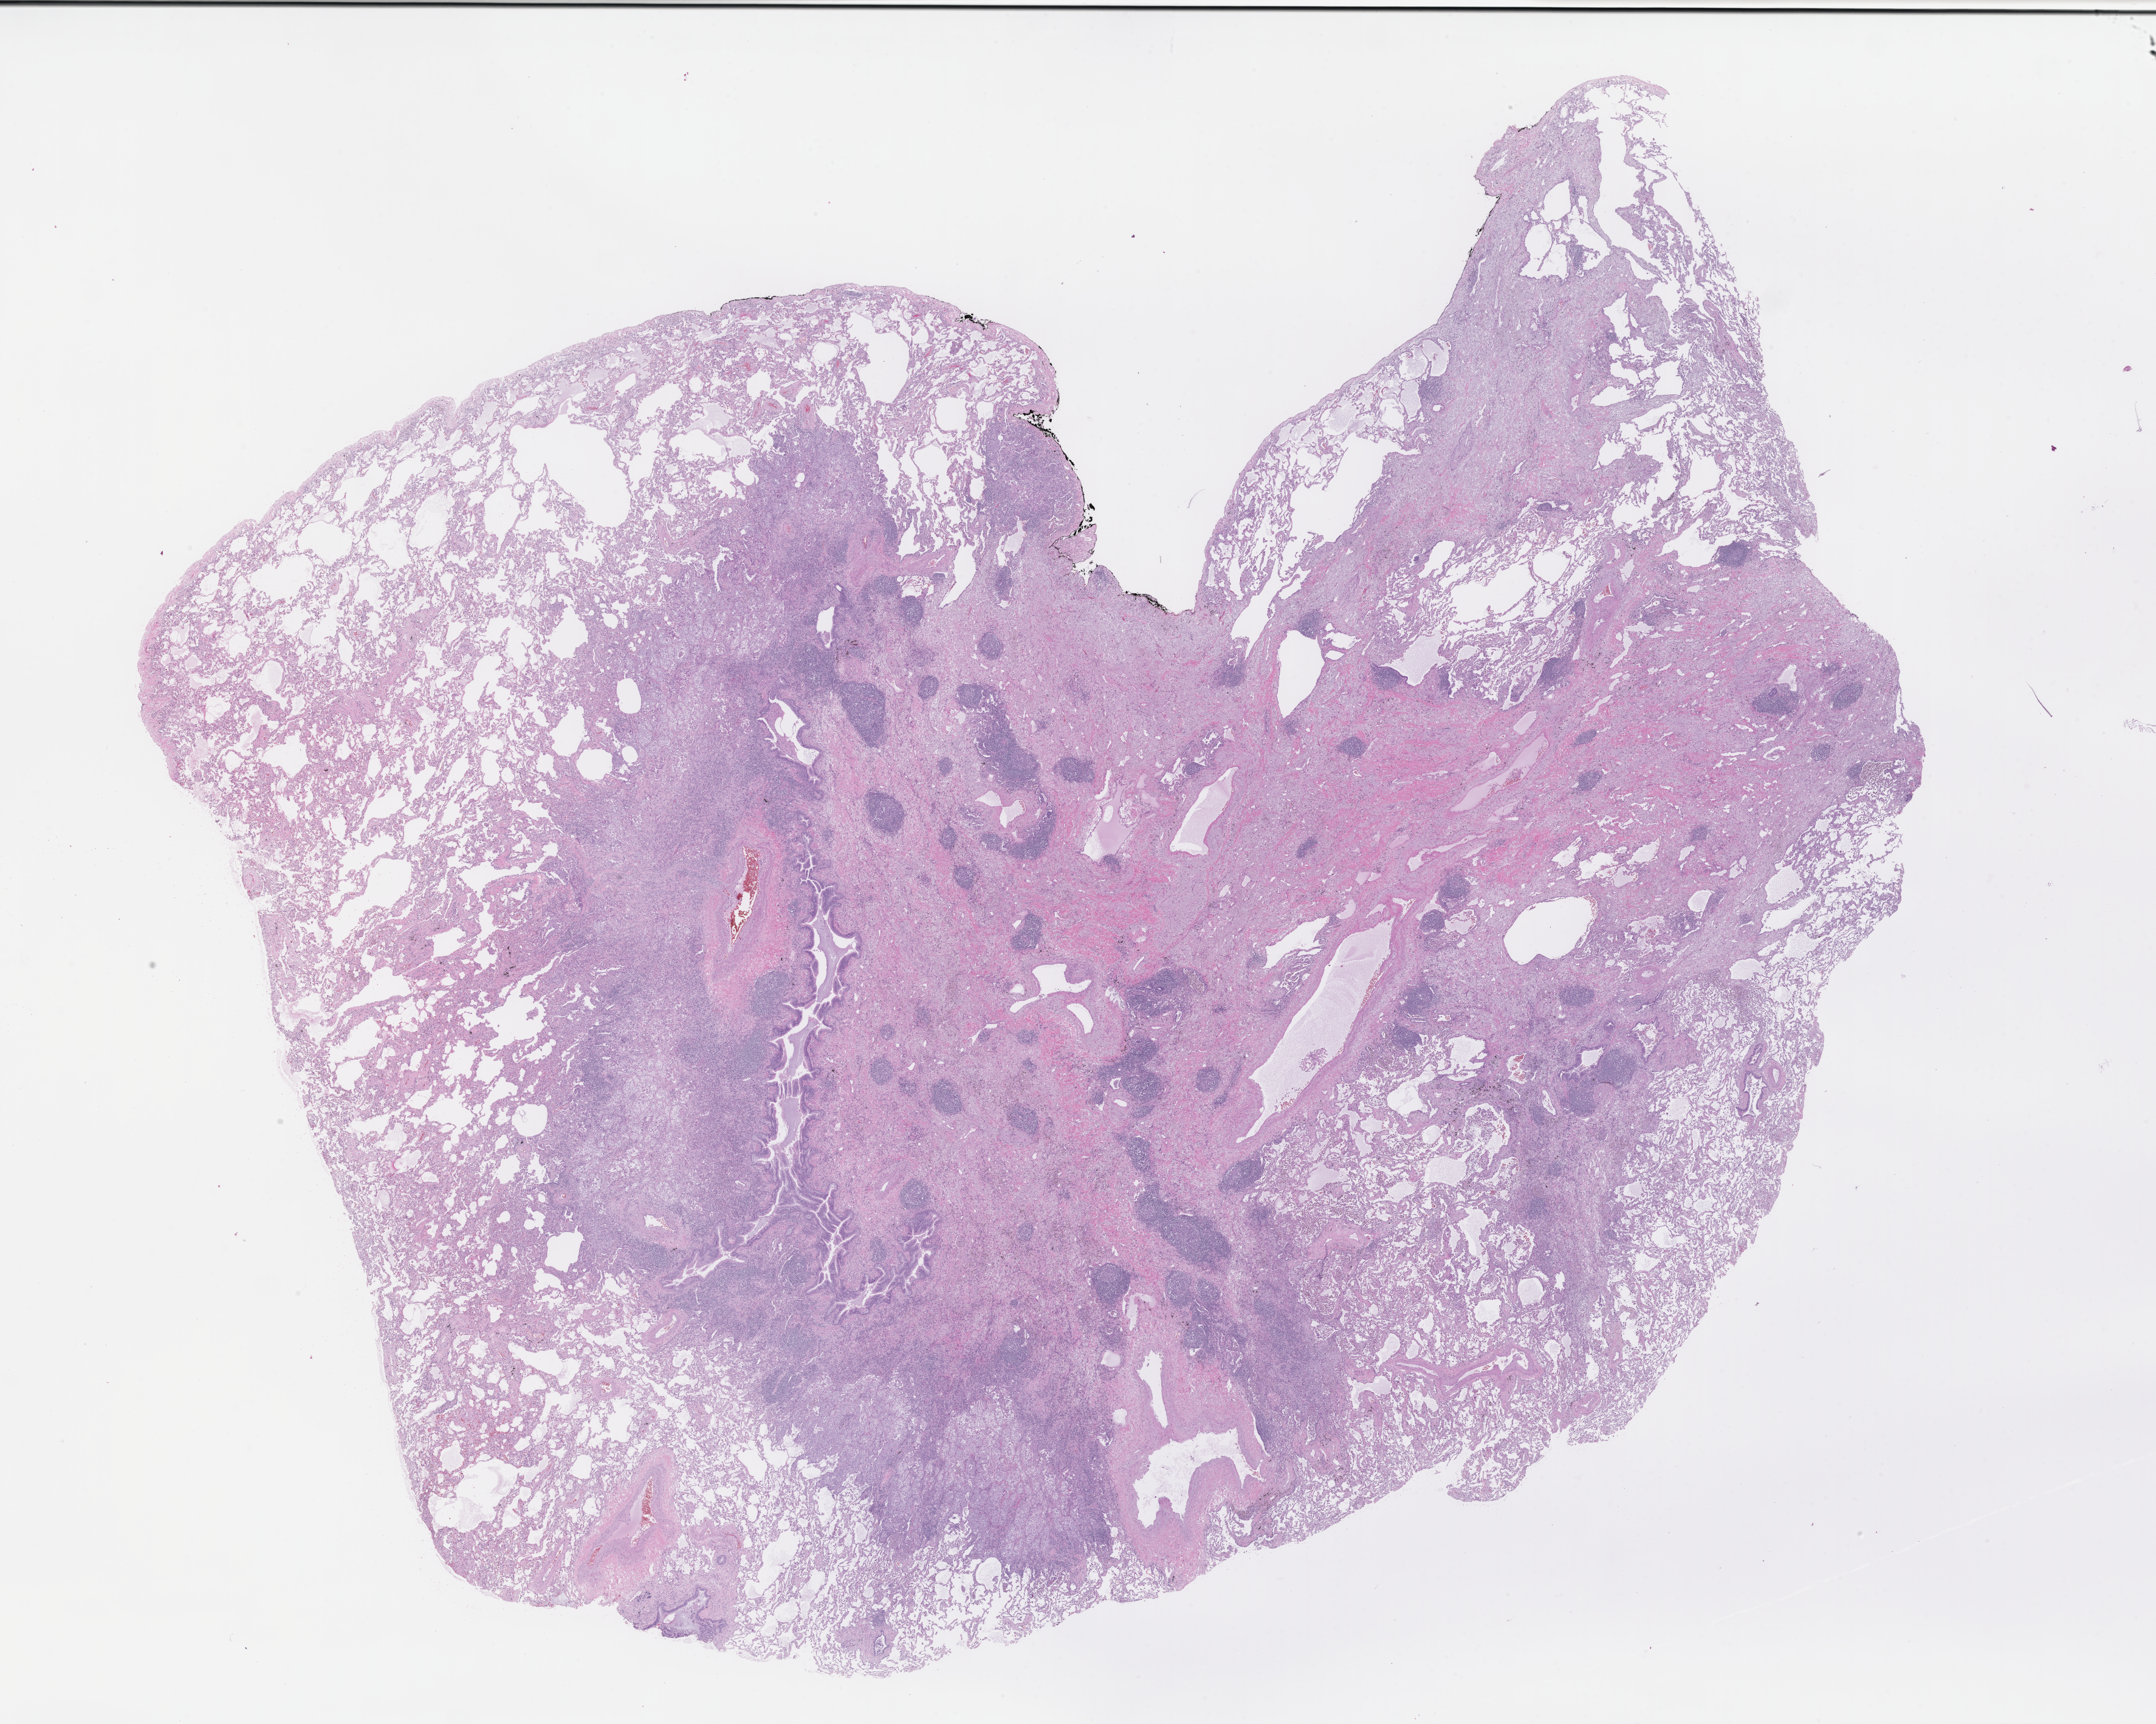
Digitized H&E-stained section, shown as a low-resolution overview of the whole scanned area (about 28.6 x 22.9 mm). Formalin-fixed, paraffin-embedded (FFPE) tissue. Tissue site: lung. Specimen time point: archival tissue. Female patient.
This section: primary tumor. Diagnosis: Non-Small Cell Lung Carcinoma.